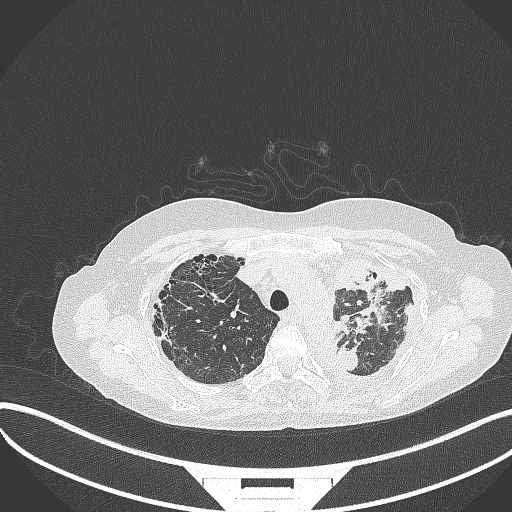
Chest CT, one axial slice. Position 264 of 373 along the scan axis. Reconstruction kernel B70f. 120 kVp. Lung window (W 1500 / L -600 HU). 1 mm slice thickness. 512 × 512 image matrix. Female patient, age 56 years. Case-level facts recorded for this patient, not image findings: clinical TNM (as recorded): T1 N0 M0.
Annotated regions visible in this slice (rectangle marked by the reading radiologist):
- lung tumour (recorded histology: adenocarcinoma): bounding box (x1, y1, x2, y2) in pixels: (338, 341, 364, 375)
- lung tumour (recorded histology: adenocarcinoma): (355, 248, 403, 330)